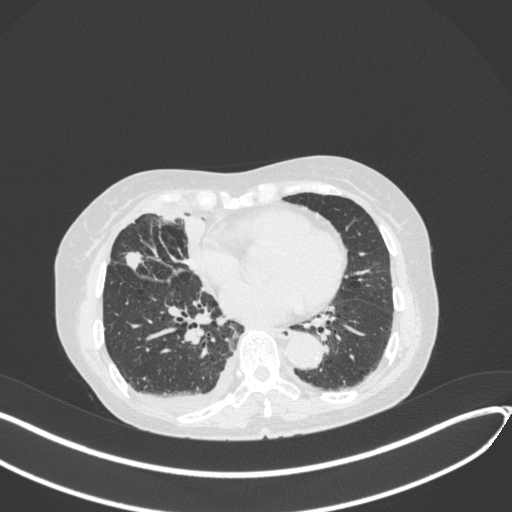
Chest CT, one axial slice; slice 161 of 418 in the series (ordered by position); reconstruction kernel B31f; 120 kVp; lung window (W 1500 / L -600 HU); 1 mm slice thickness; 512 × 512 image matrix. Female patient, age 75 years. From the clinical record (not read from this slice): clinical TNM (as recorded): T2a N3 M0.
Structures marked on this image (rectangle marked by the reading radiologist):
- lung tumour (recorded histology: adenocarcinoma): bounding box (x1, y1, x2, y2) in pixels: (124, 250, 148, 277)